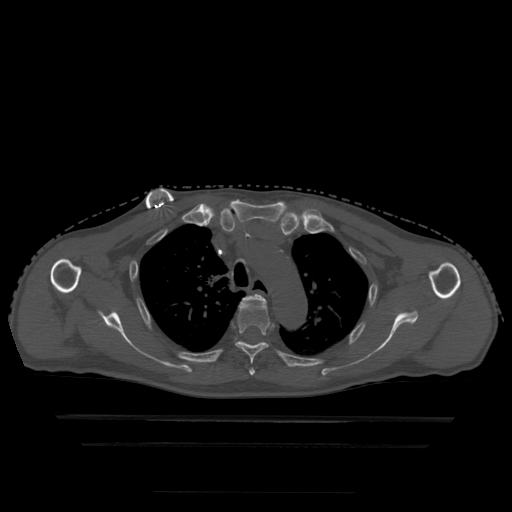
CT including the spine, one axial slice; bone window (W 1800 / L 400 HU); 1.25 mm slice thickness; 512 × 512 image matrix, field of view 436 × 436 mm. Patient age 68 years. Case-level facts recorded for this patient, not image findings: primary cancer: urothelial.
Annotated regions visible in this slice (semi-automatic segmentation, software-assisted and operator-edited):
- T3 vertebra: bounding box <242,294,266,375> (left, top, right, bottom; pixels)
- T4 vertebra: <236,297,270,376>